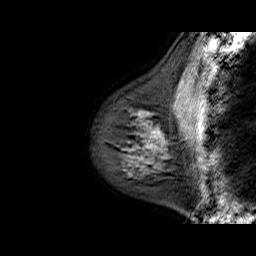
Breast MRI (dynamic contrast-enhanced), one sagittal slice. Position 18 of 60 along the scan axis. Dynamic contrast-enhanced series, time point 2 of 6 at this slice position (early post-contrast). 1.5 T. TE 6.4 ms, TR 32.9 ms. 256 × 256 image matrix. Female patient. Case-level facts recorded for this patient, not image findings: setting: breast cancer imaged before/during neoadjuvant chemotherapy; receptor status: HR-positive, HER2-negative.
Outlined on this slice (semi-automatic segmentation, software-assisted and operator-edited):
- analysis volume of interest (the breast-tissue region the enhancement analysis was run in; not a lesion): bounding box [x1, y1, x2, y2] px = [105, 107, 168, 175]
- tumour enhancement mask (voxels above the 100 % enhancement threshold inside the analysis volume of interest): [152, 129, 160, 137]